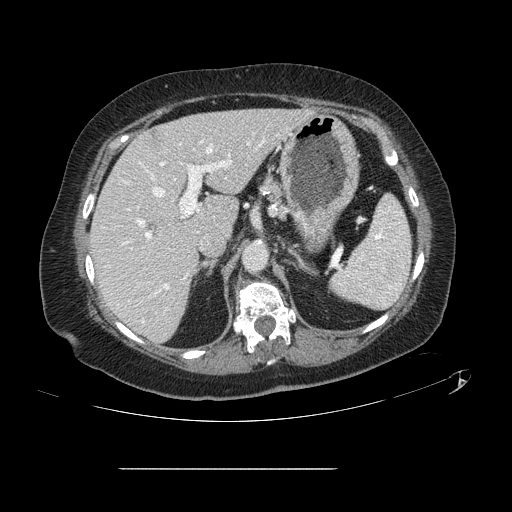
Contrast-enhanced abdominal CT, one axial slice; position 83 of 148 along the scan axis; intravenous contrast given; soft-tissue window (W 400 / L 40 HU); 2.5 mm slice thickness; 512 × 512 image matrix, field of view 439 × 439 mm. Female patient, age 75 years. From the clinical record (not read from this slice): diagnosis: colorectal cancer liver metastases, imaged before liver resection; multiple liver metastases: no; largest metastasis: 2.4 cm; disease in both lobes: no.
Annotated regions visible in this slice (outlined manually by an expert reader):
- hepatic veins: bounding box <142,148,212,322> (left, top, right, bottom; pixels)
- liver: <90,109,308,342>
- planned liver remnant (the part of the liver to remain after resection): <91,109,309,342>
- portal vein (with intrahepatic branches): <137,133,266,289>
- liver metastasis: <152,133,159,145>